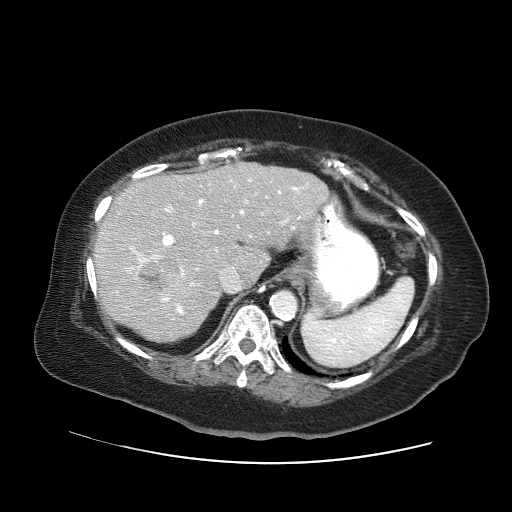
Contrast-enhanced abdominal CT (liver protocol), one axial slice; reconstruction kernel STANDARD; 120 kVp; soft-tissue window (W 400 / L 40 HU); 2.5 mm slice thickness; 512 × 512 image matrix, field of view 400 × 400 mm. From the clinical record (not read from this slice): diagnosis: hepatocellular carcinoma (patient treated with transarterial chemoembolisation; whether this scan precedes or follows treatment is not stated here); TNM stage (as recorded): Stage-II; Child-Pugh class: A; tumour differentiation: poorly differentiated; tumour size: 5 cm.
Annotated regions visible in this slice (semi-automatically segmented with operator editing):
- liver parenchyma outside the tumour (the mass and vessels are separate outlines, so this box may not span the whole liver): bounding box <94,162,328,342> (left, top, right, bottom; pixels)
- mass: <136,258,184,298>
- liver vessels: <101,180,308,315>